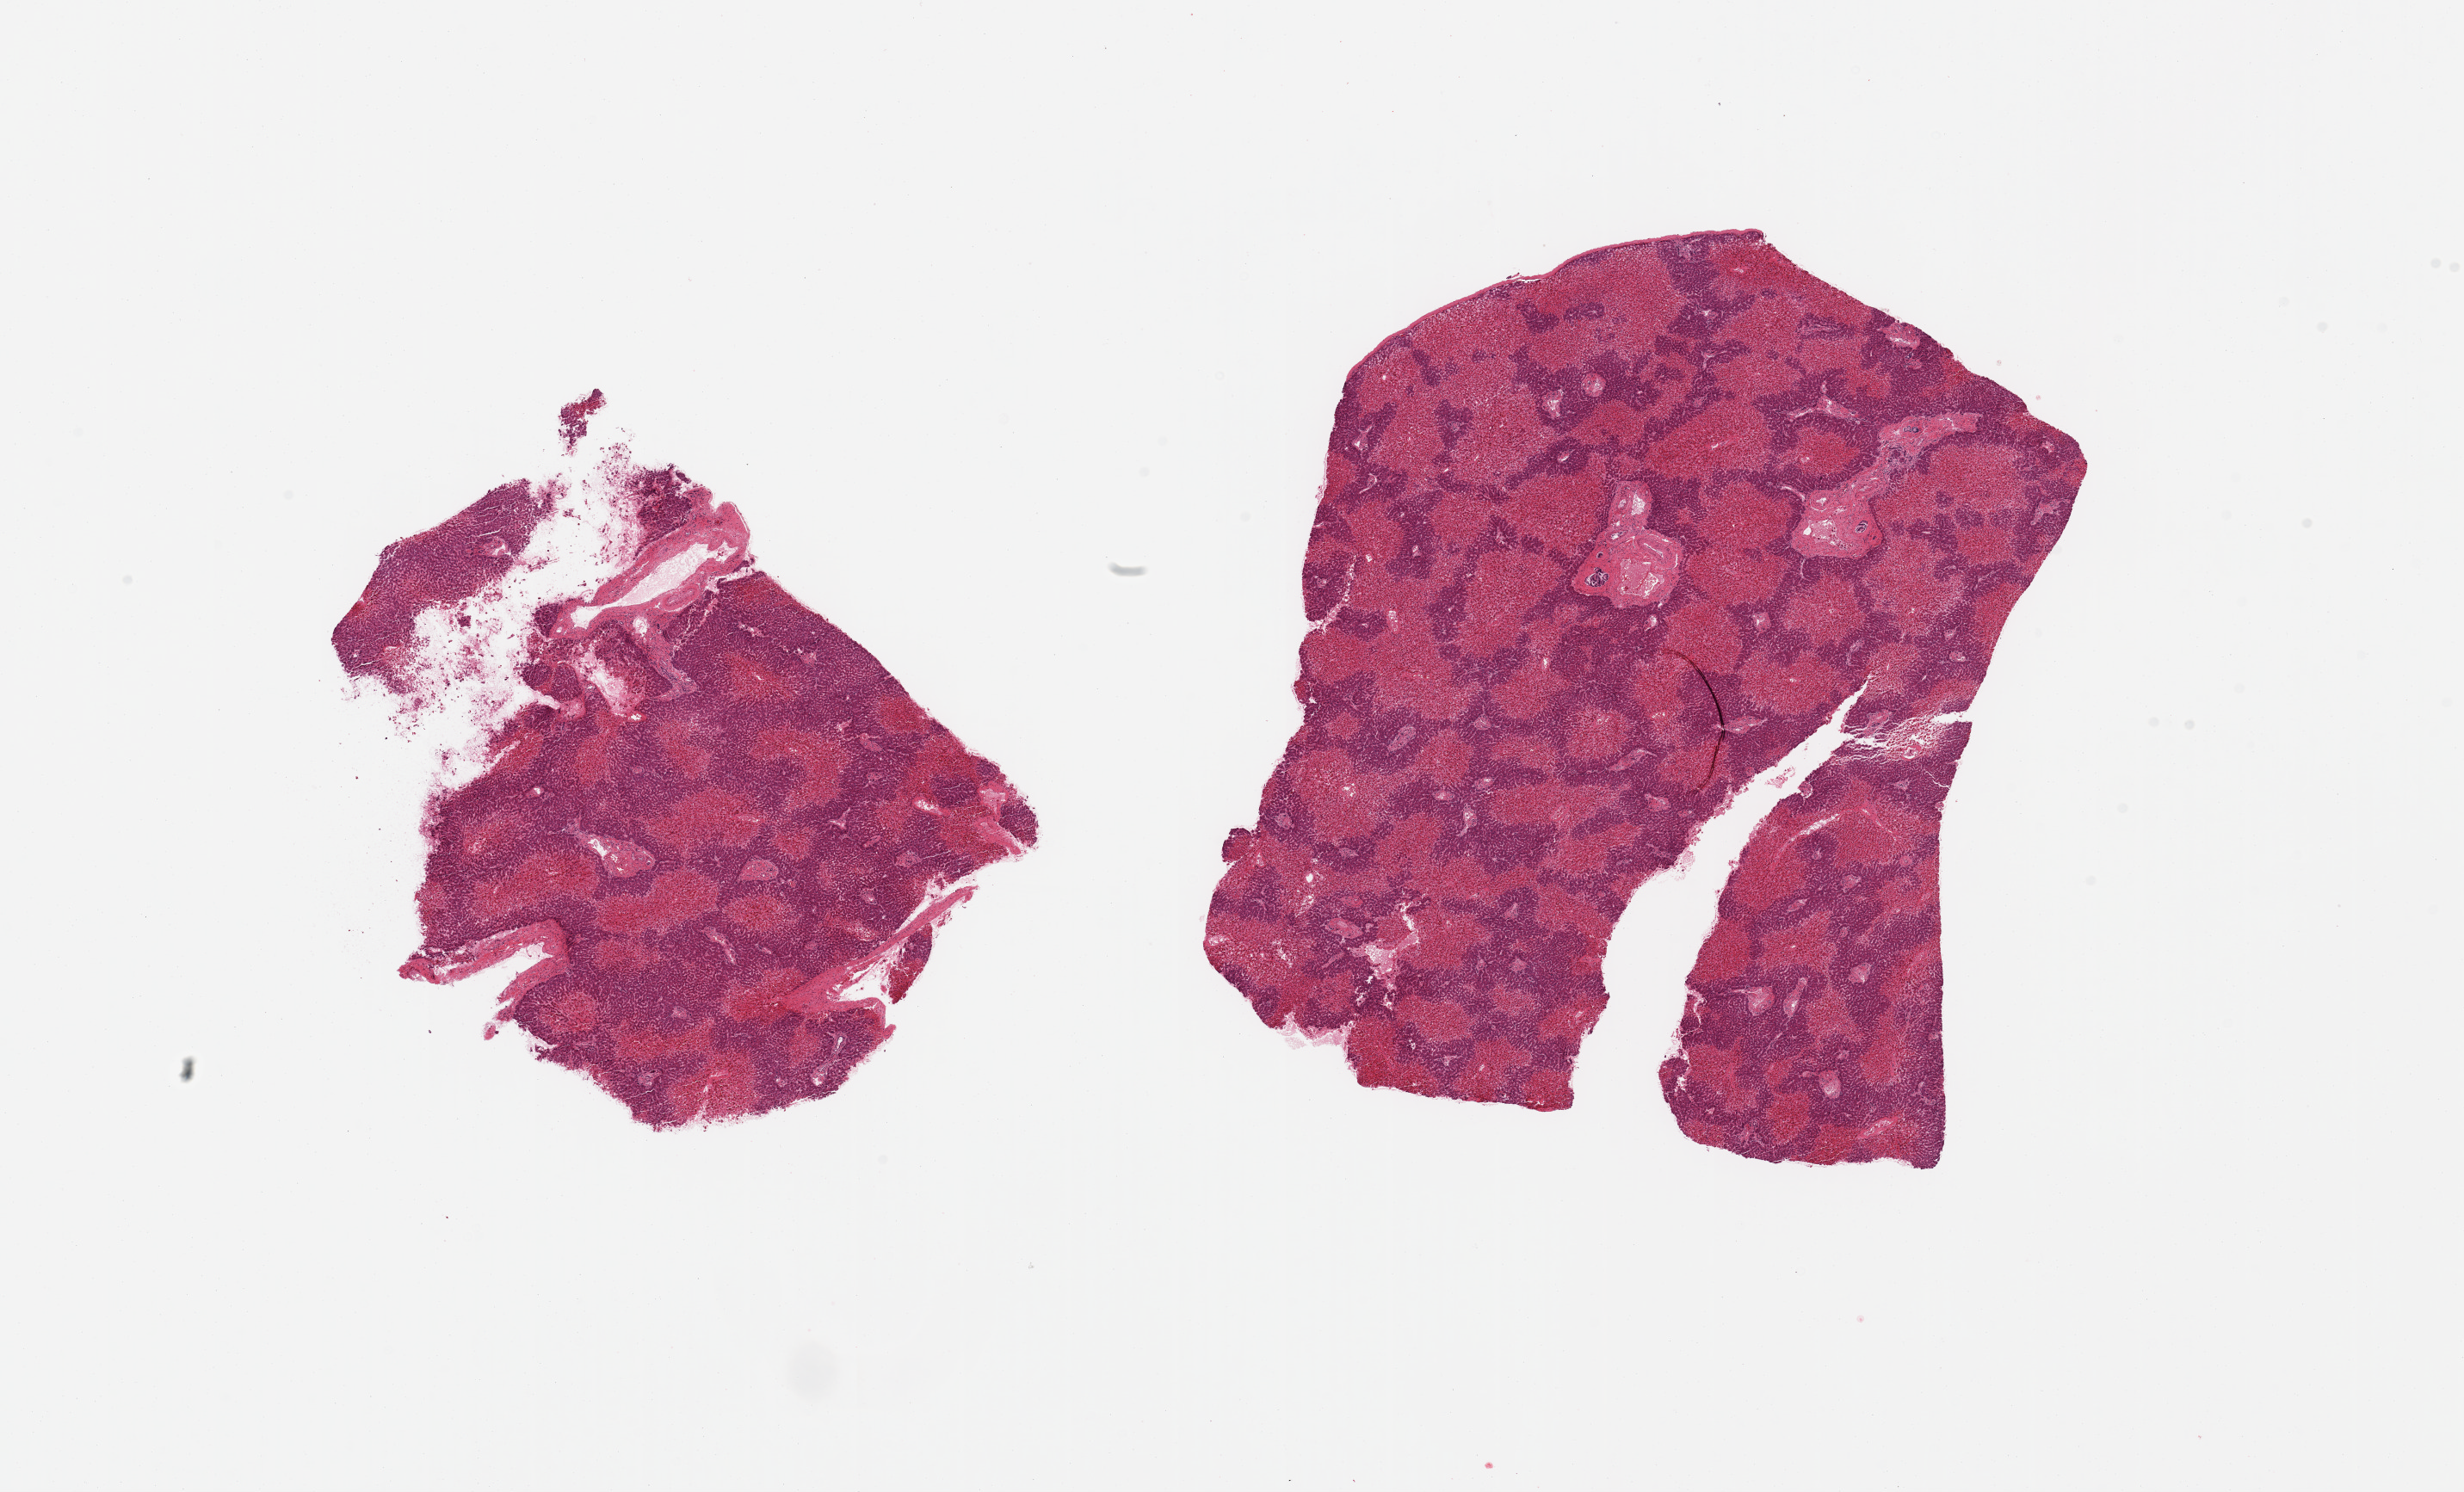
Digitized haematoxylin and eosin-stained section — a low-resolution overview of the entire scanned area, about 22.6 x 13.7 mm; PAXgene-fixed, paraffin-embedded tissue; sampled site (target tissue): liver; donor tissue sample. Donor sex: male.
Review note (as recorded): 2 pieces; severe central congestion & degeneration.